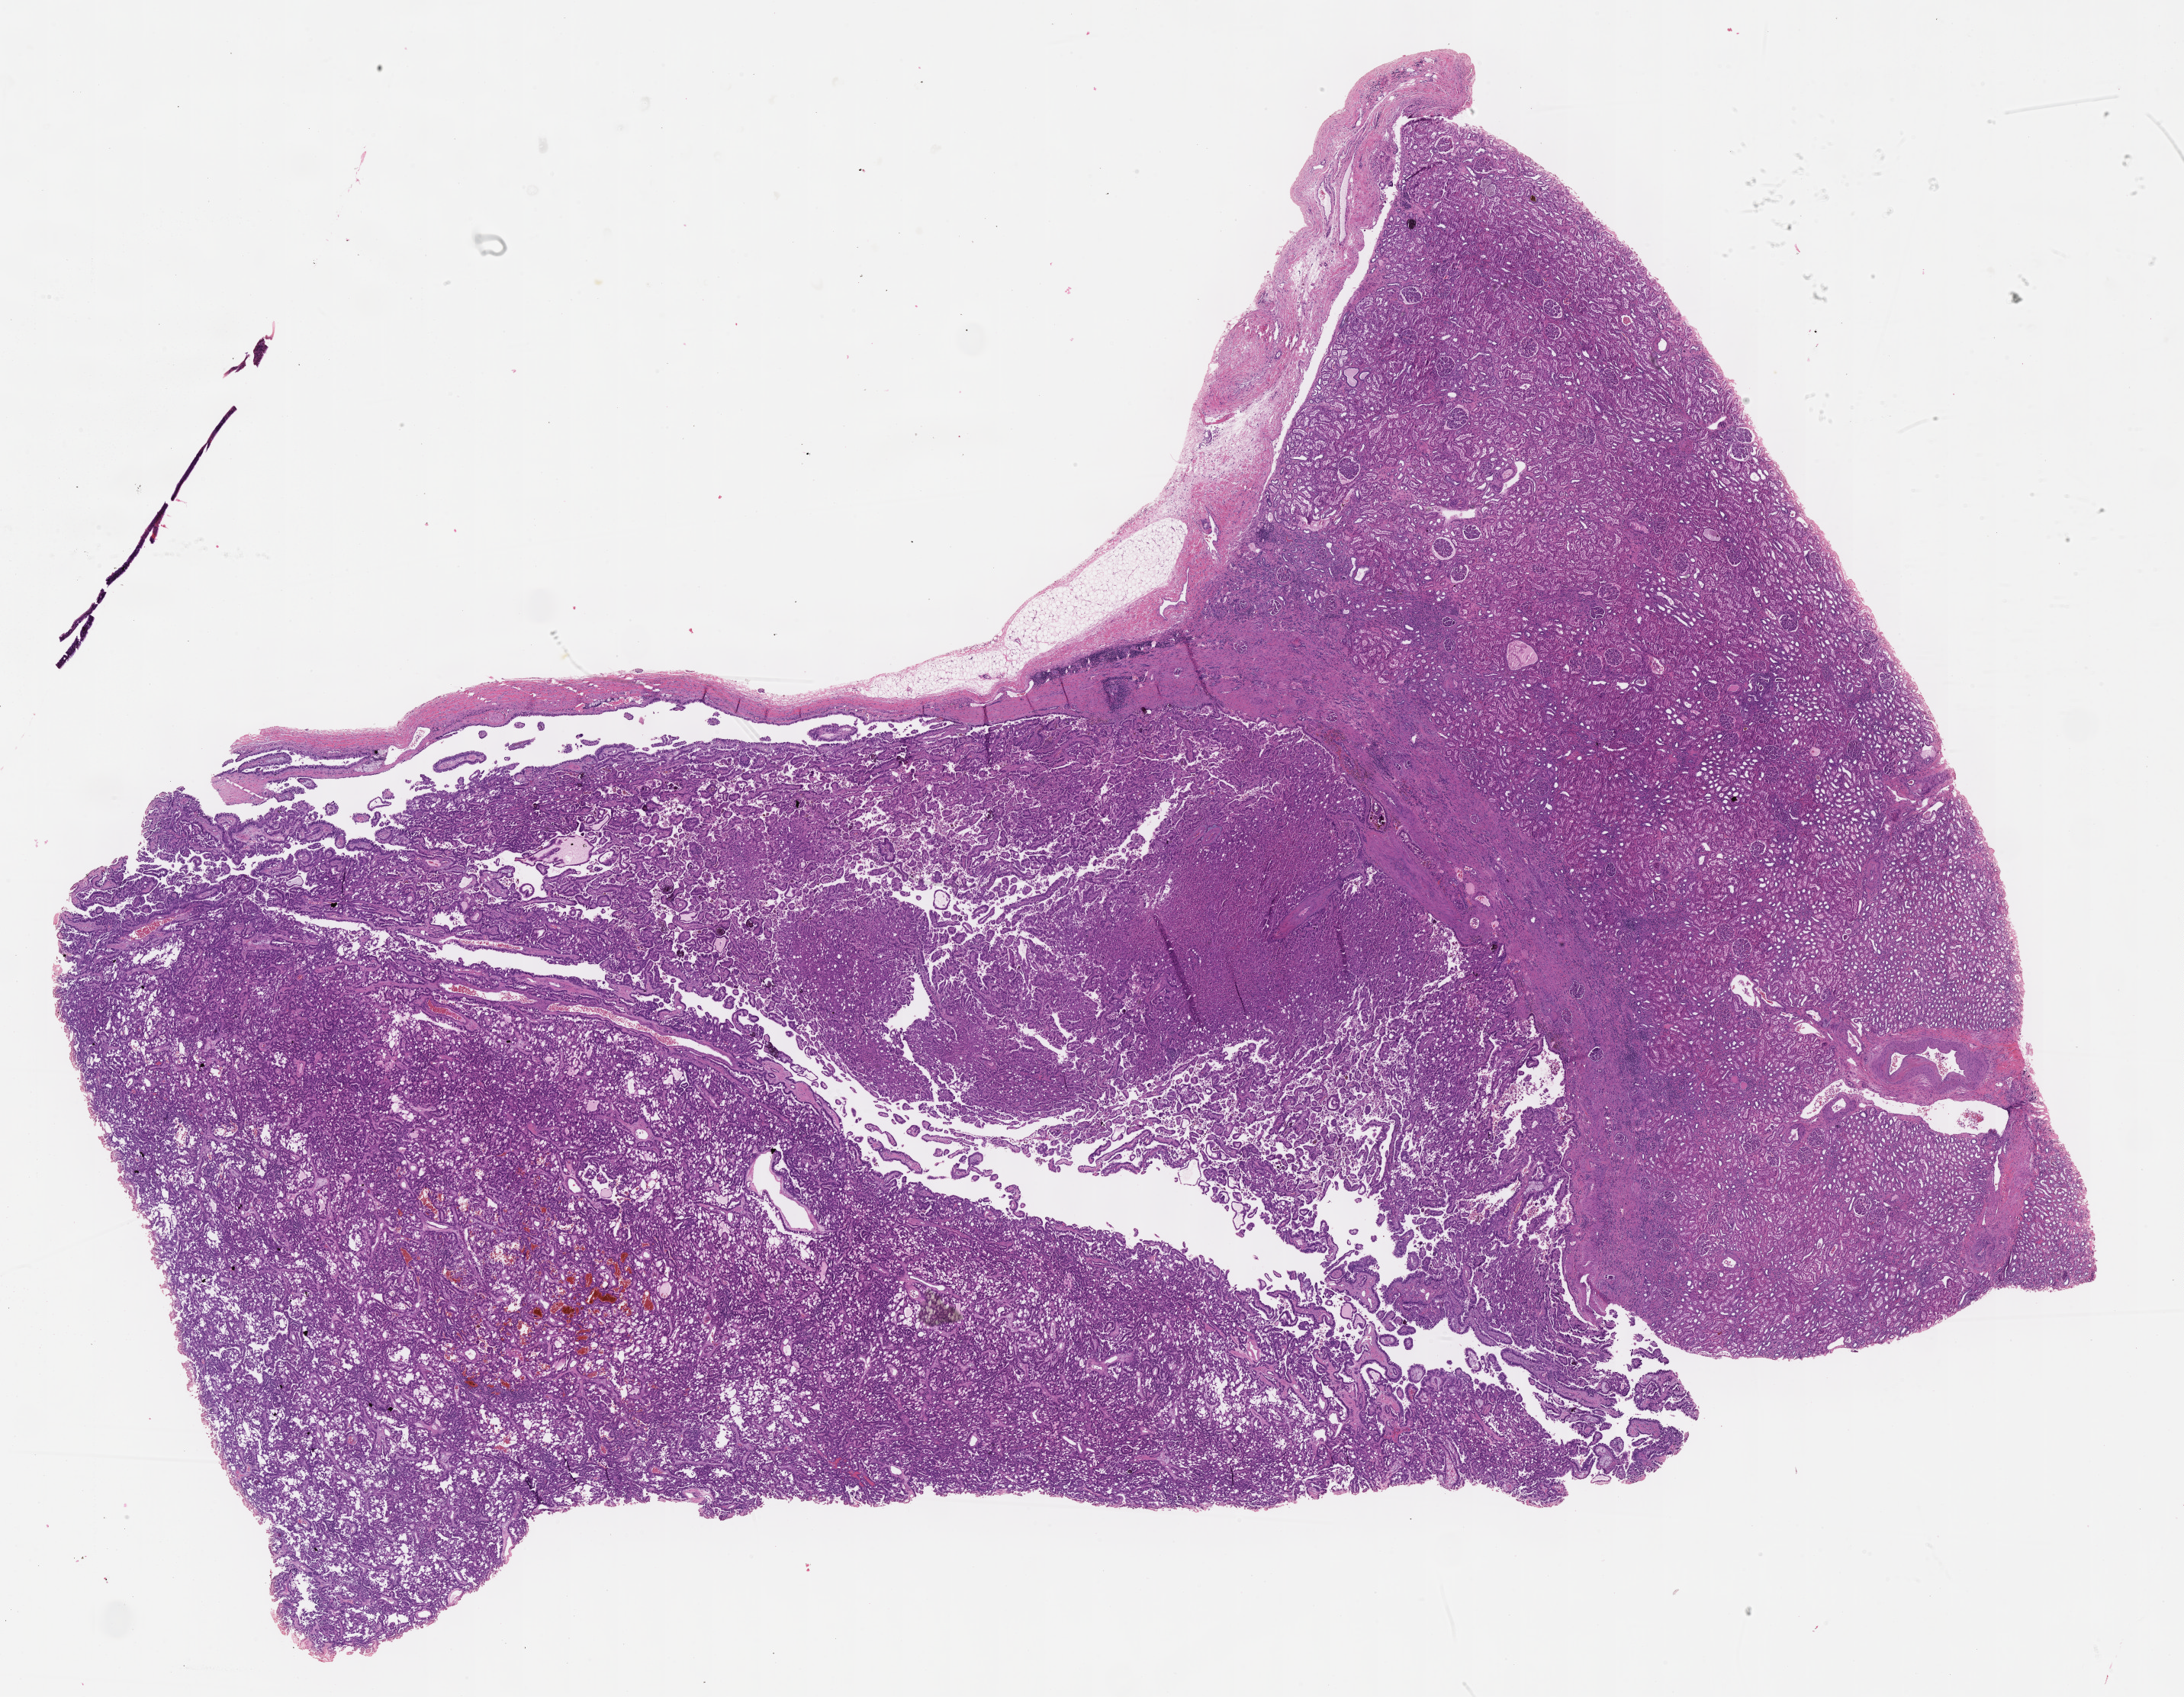
Digitized H&E tissue section (whole slide) — a low-resolution overview of the entire scanned area, about 23.1 x 18.0 mm (slide scanned at 40x); formalin-fixed paraffin-embedded (FFPE) diagnostic section; kidney, primary tumour sample. Patient sex: male.
Pathologic diagnosis: Papillary adenocarcinoma, NOS. AJCC pathologic stage: I (7th edition).